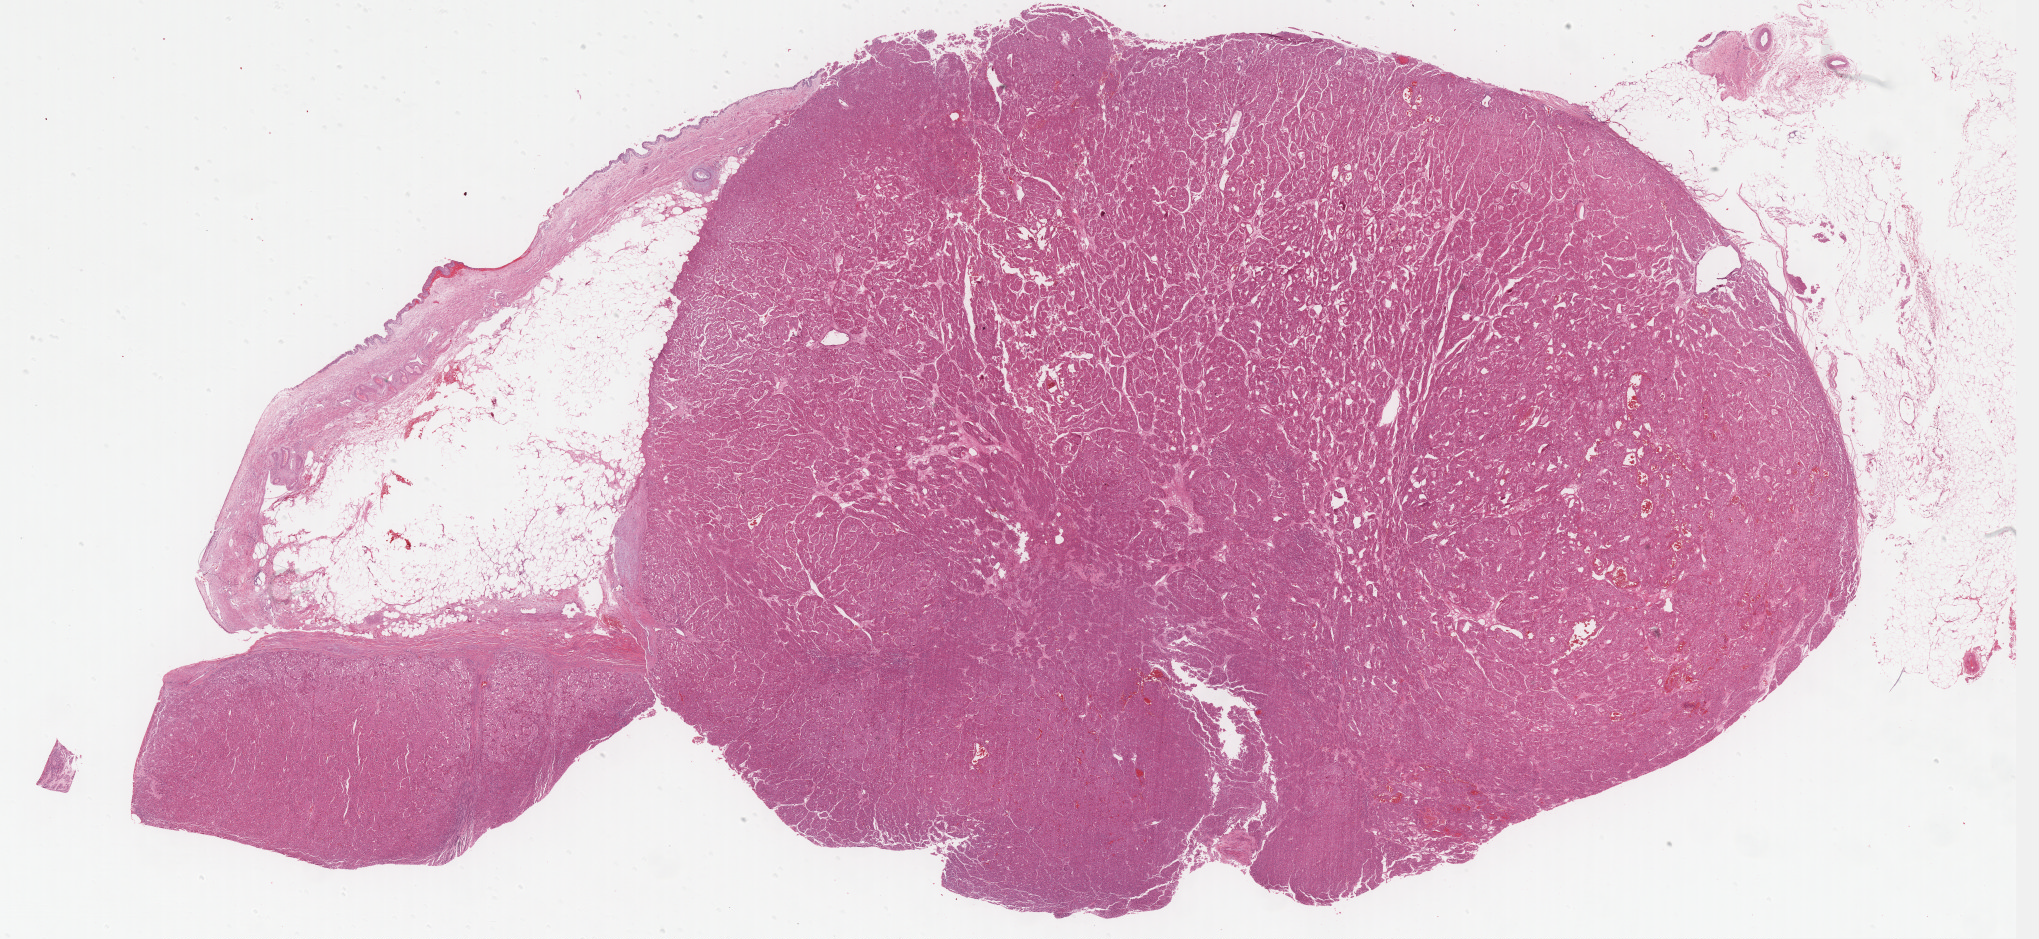
Whole-slide histology image, H&E — low-resolution overview of the scanned area, about 32.6 x 15.0 mm (acquisition: 40x scan); formalin-fixed paraffin-embedded (FFPE) diagnostic section; kidney, primary tumour sample. Male, age 51 years at initial diagnosis.
Diagnosis: Renal cell carcinoma, chromophobe type. AJCC pathologic stage: III (6th edition). Laterality: right.